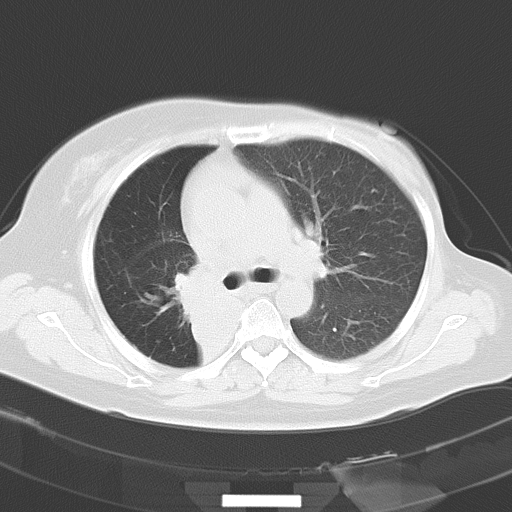
Chest CT, one axial slice; position 20 of 30 along the scan axis; reconstruction kernel B70f; 120 kVp; lung window (W 1500 / L -600 HU); 512 × 512 image matrix, field of view 331 × 331 mm. Female patient, age 53 years. Case-level facts recorded for this patient, not image findings: clinical TNM (as recorded): T2b N1 M0.
Annotated regions visible in this slice (rectangle marked by the reading radiologist):
- lung tumour (recorded histology: adenocarcinoma): bounding box <171,256,228,340> (left, top, right, bottom; pixels)